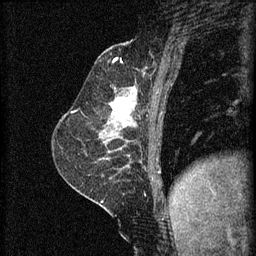
Breast MRI (dynamic contrast-enhanced), one sagittal slice. Position 24 of 60 along the scan axis. 3 images stored at this slice position (order not interpretable as contrast timing). 1.5 T. TE 4.2 ms, TR 8.2 ms. 256 × 256 image matrix, field of view 180 × 180 mm. Patient: female, 59 years.
Annotated regions visible in this slice (semi-automatic segmentation, software-assisted and operator-edited):
- analysis volume of interest (the breast-tissue region the enhancement analysis was run in; not a lesion): bounding box <100,92,137,135> (left, top, right, bottom; pixels)
- tumour enhancement mask (voxels above the 70 % enhancement threshold inside the analysis volume of interest): <110,92,137,123>